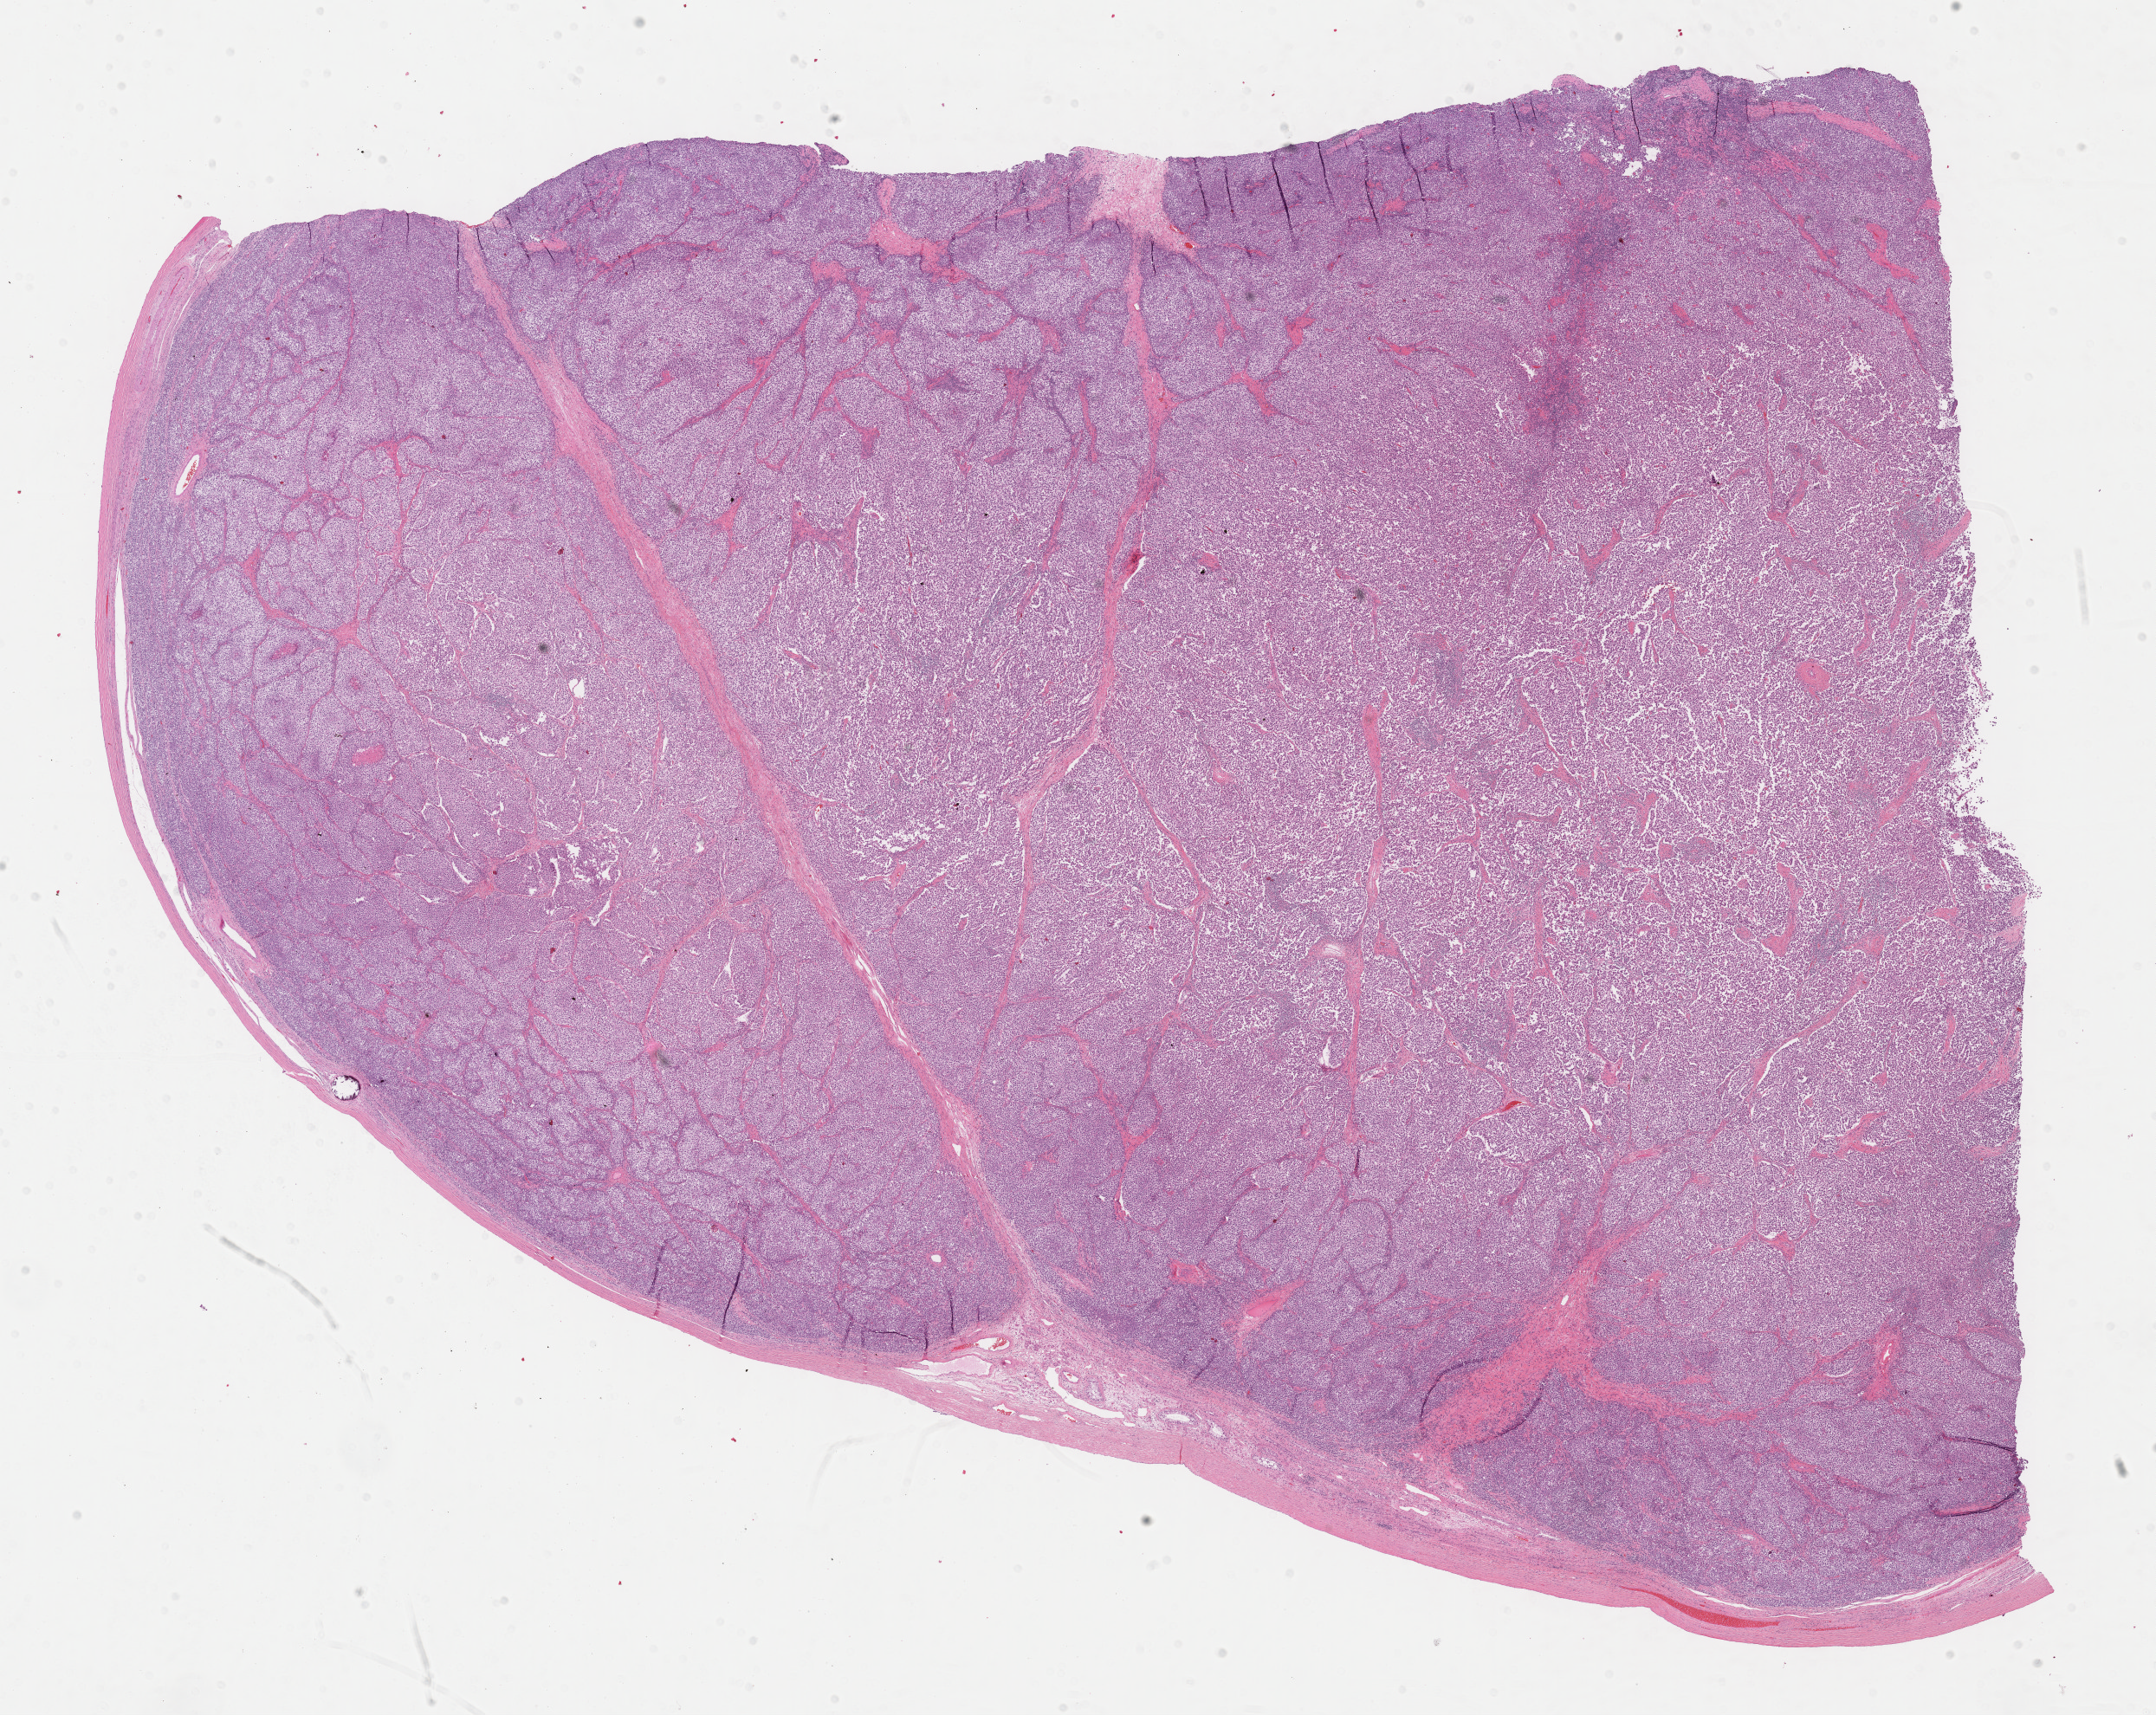
H&E whole-slide image, a low-resolution overview of the entire scanned area, about 20.1 x 16.0 mm (from a 40x scan); formalin-fixed paraffin-embedded (FFPE) diagnostic section; testis, primary tumour sample. Male, age 38 years at initial diagnosis.
Diagnosis: Seminoma, NOS.